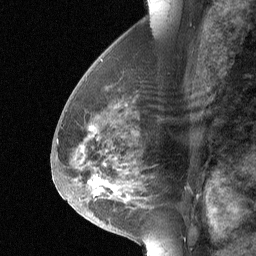
Breast MRI (dynamic contrast-enhanced), one sagittal slice; position 31 of 64 along the scan axis; dynamic contrast-enhanced study with each time point stored as its own series, time point 2 of 3 at this slice position (early post-contrast, ordered by acquisition time); 1.5 T; TE 4.8 ms, TR 27 ms; 256 × 256 image matrix. Female patient, age 56 years. From the clinical record (not read from this slice): setting: breast cancer imaged before/during neoadjuvant chemotherapy; receptor status: HER2-positive.
Annotated regions visible in this slice (semi-automatically segmented with operator editing):
- analysis volume of interest (the breast-tissue region the enhancement analysis was run in; not a lesion): bounding box <68,83,154,214> (left, top, right, bottom; pixels)
- tumour enhancement mask (voxels above the 90 % enhancement threshold inside the analysis volume of interest): <89,177,110,195>